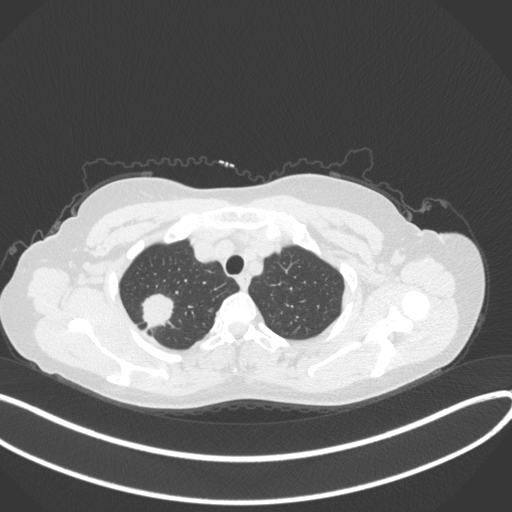
Chest CT, one axial slice. Slice 311 of 342 in the series (ordered by position). Reconstruction kernel B31f. 120 kVp. Lung window (W 1500 / L -600 HU). 1 mm slice thickness. 512 × 512 image matrix, field of view 400 × 400 mm. Female patient, age 50 years. From the clinical record (not read from this slice): clinical TNM (as recorded): T1c N0 M0; histopathological grade: G2-3.
Structures marked on this image (bounding box drawn by a radiologist):
- lung tumour (recorded histology: adenocarcinoma): bounding box [x1, y1, x2, y2] px = [136, 289, 177, 332]